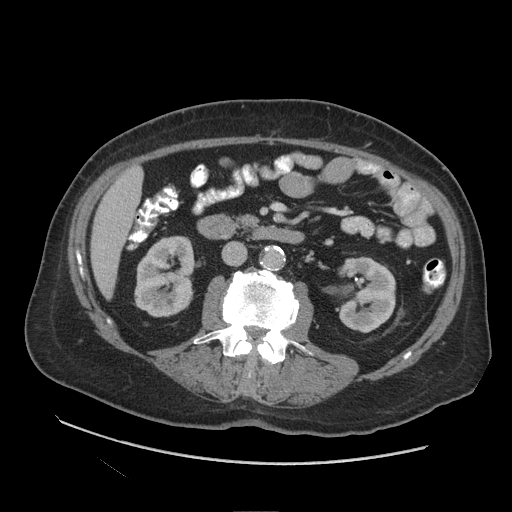
Contrast-enhanced abdominal CT (liver protocol), one axial slice. Position 29 of 109 along the scan axis. Soft-tissue window (W 400 / L 40 HU). 512 × 512 image matrix. Case-level facts recorded for this patient, not image findings: diagnosis: hepatocellular carcinoma (patient treated with transarterial chemoembolisation; whether this scan precedes or follows treatment is not stated here); TNM stage (as recorded): Stage-I; Child-Pugh class: A.
Annotated regions visible in this slice (semi-automatic segmentation, software-assisted and operator-edited):
- liver parenchyma outside the tumour (the mass and vessels are separate outlines, so this box may not span the whole liver): bounding box [x1, y1, x2, y2] px = [90, 168, 142, 298]